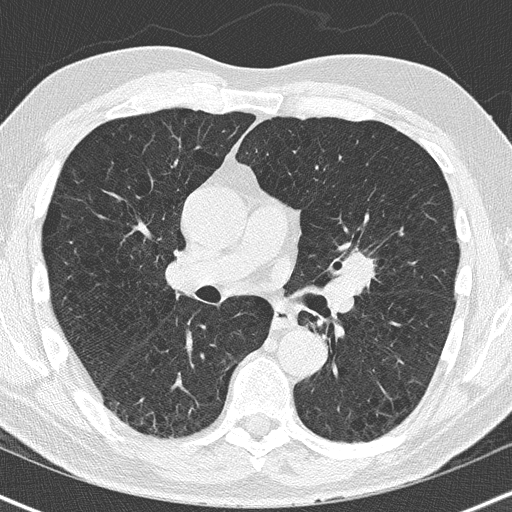
Low-dose screening chest CT, one axial slice; position 88 of 163 along the scan axis; 120 kVp; lung window (W 1500 / L -600 HU); 2 mm slice thickness; 512 × 512 image matrix, field of view 320 × 320 mm.
Annotated regions visible in this slice (outlined manually by an expert reader):
- lesion 1 (tumor, upper lobe of left lung): bounding box (x1, y1, x2, y2) in pixels: (341, 252, 376, 296)